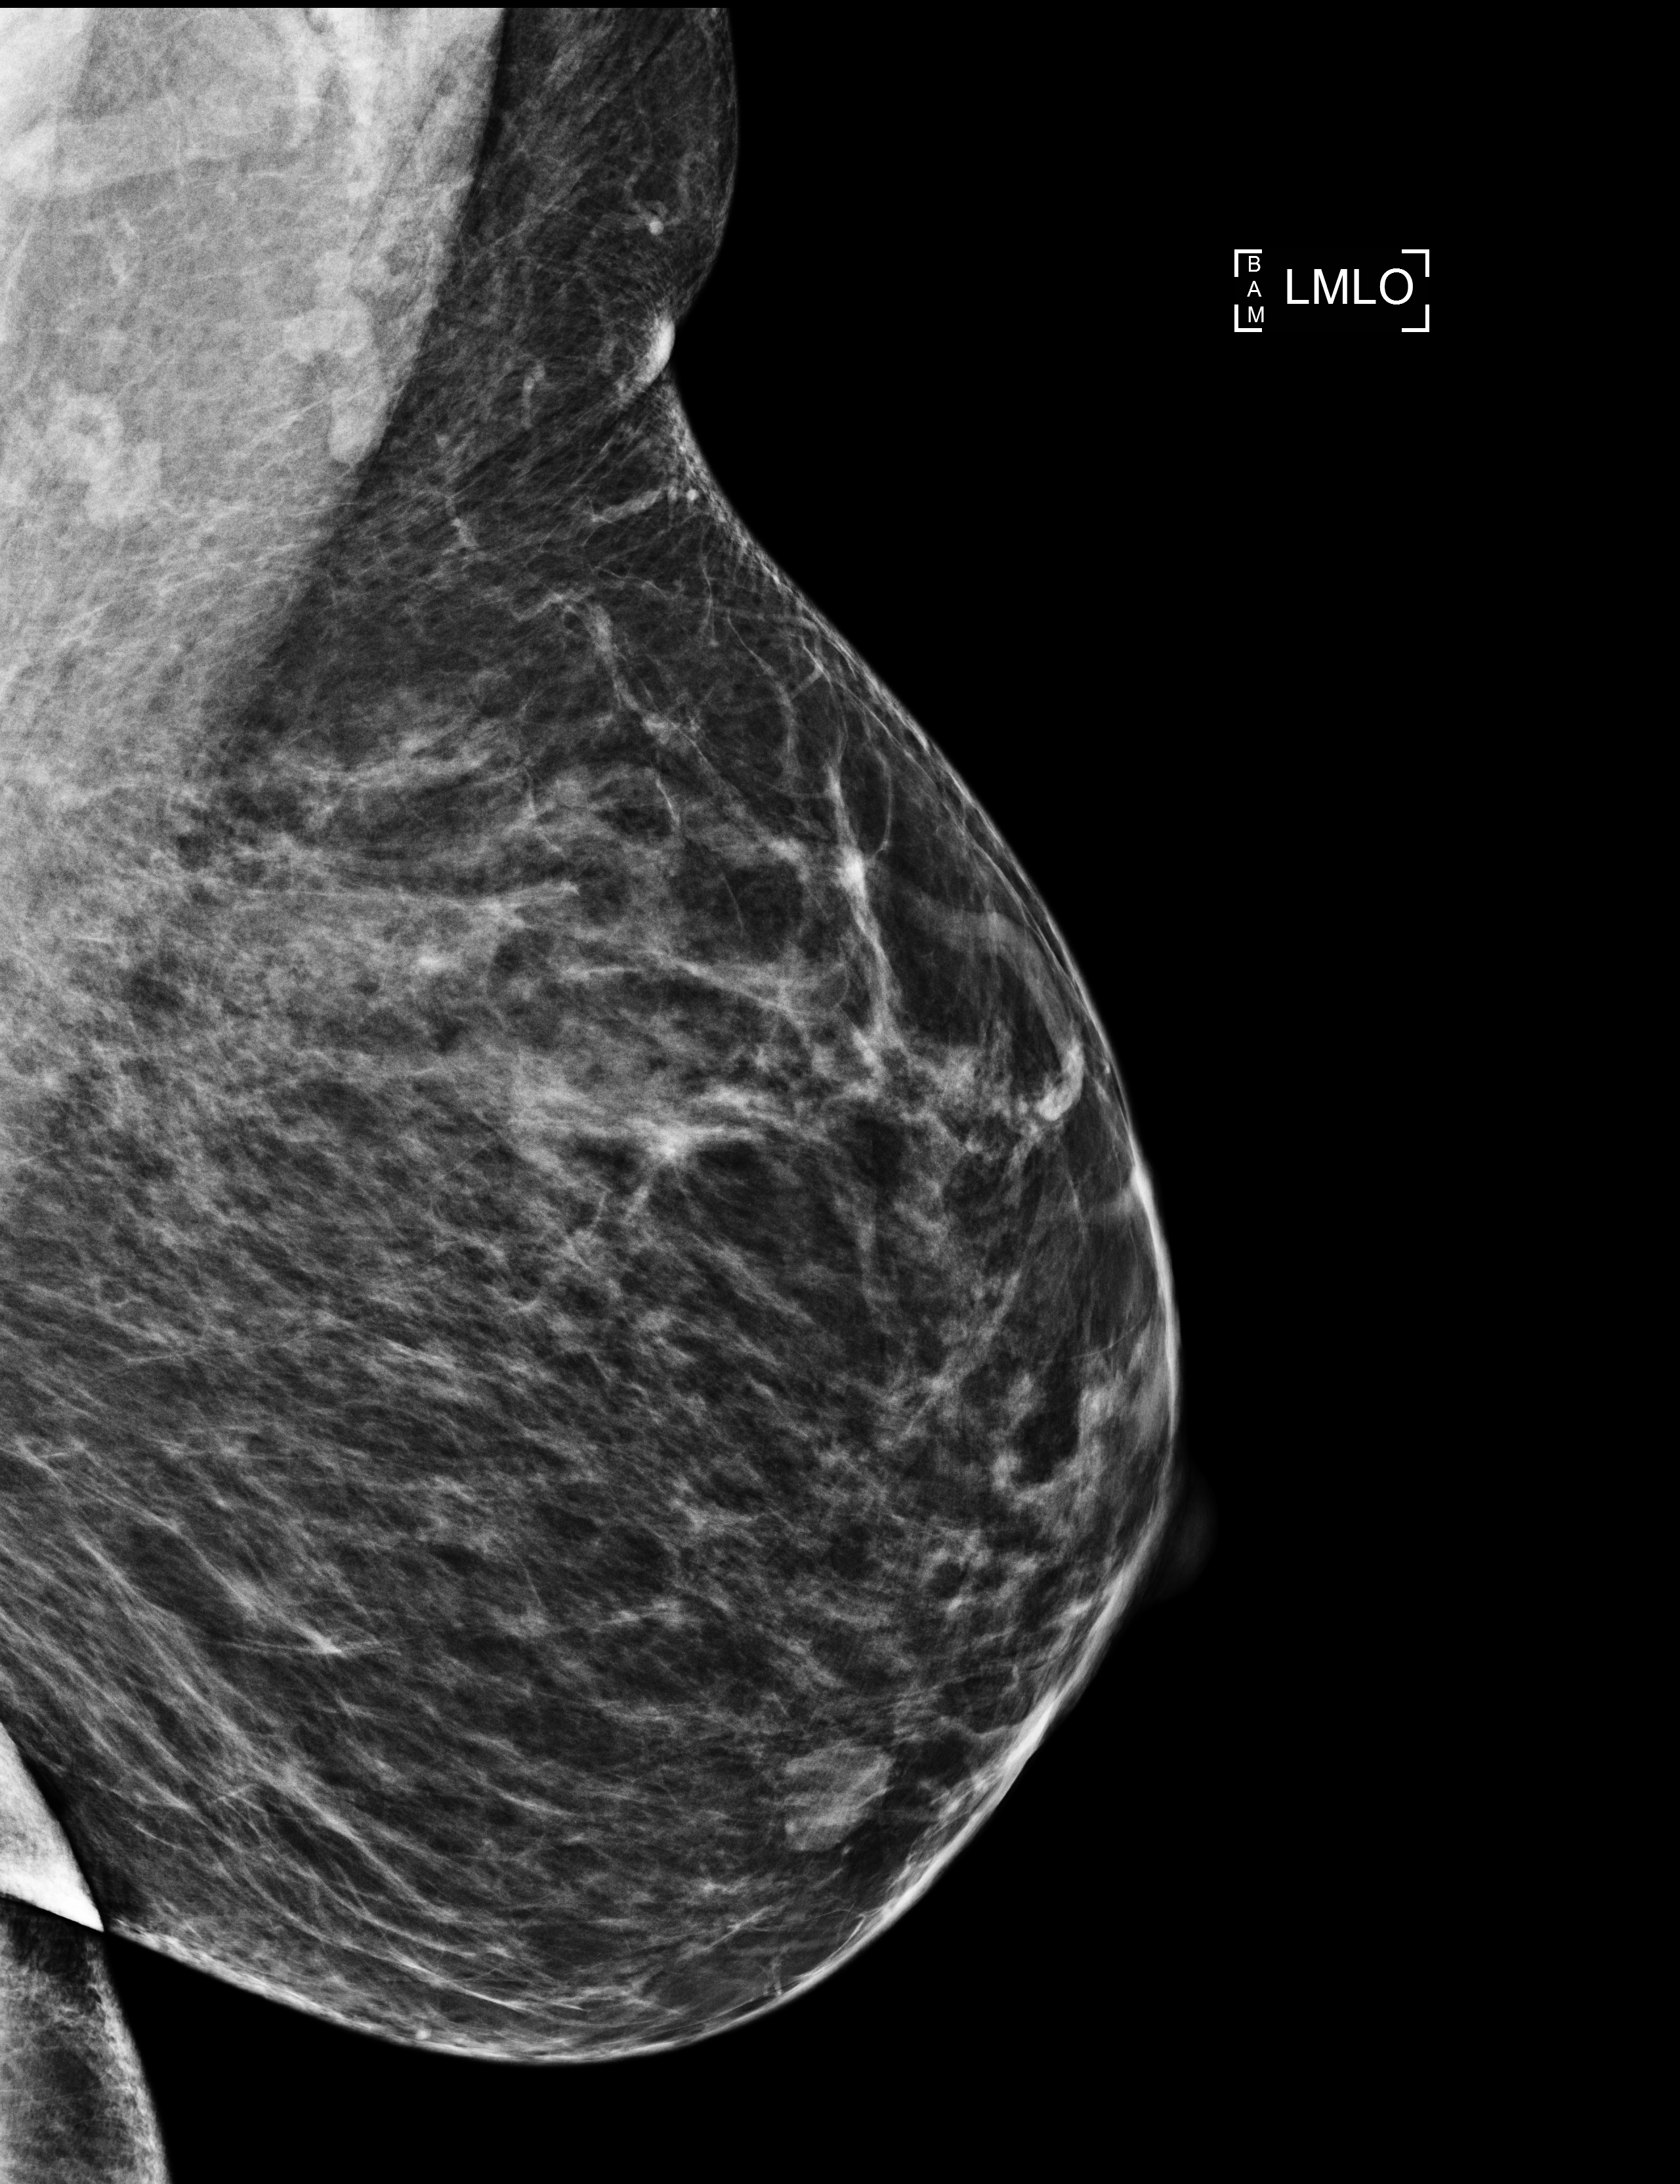
Screening examination. Patient: female, 45 years.
Image type: full-field digital mammogram. Breast: left. Projection: medio-lateral oblique projection.